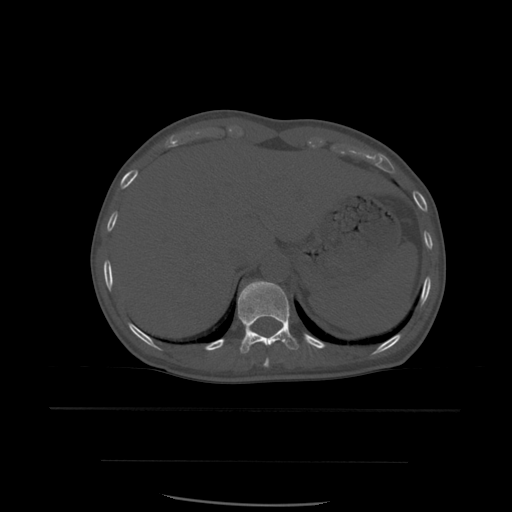
CT including the spine, one axial slice; bone window (W 1800 / L 400 HU); 1.25 mm slice thickness; 512 × 512 image matrix. Patient age 48 years. From the clinical record (not read from this slice): primary cancer: lung.
Annotated regions visible in this slice (semi-automatic segmentation, software-assisted and operator-edited):
- T10 vertebra: bounding box (x1, y1, x2, y2) in pixels: (264, 358, 270, 368)
- T11 vertebra: (238, 281, 299, 354)